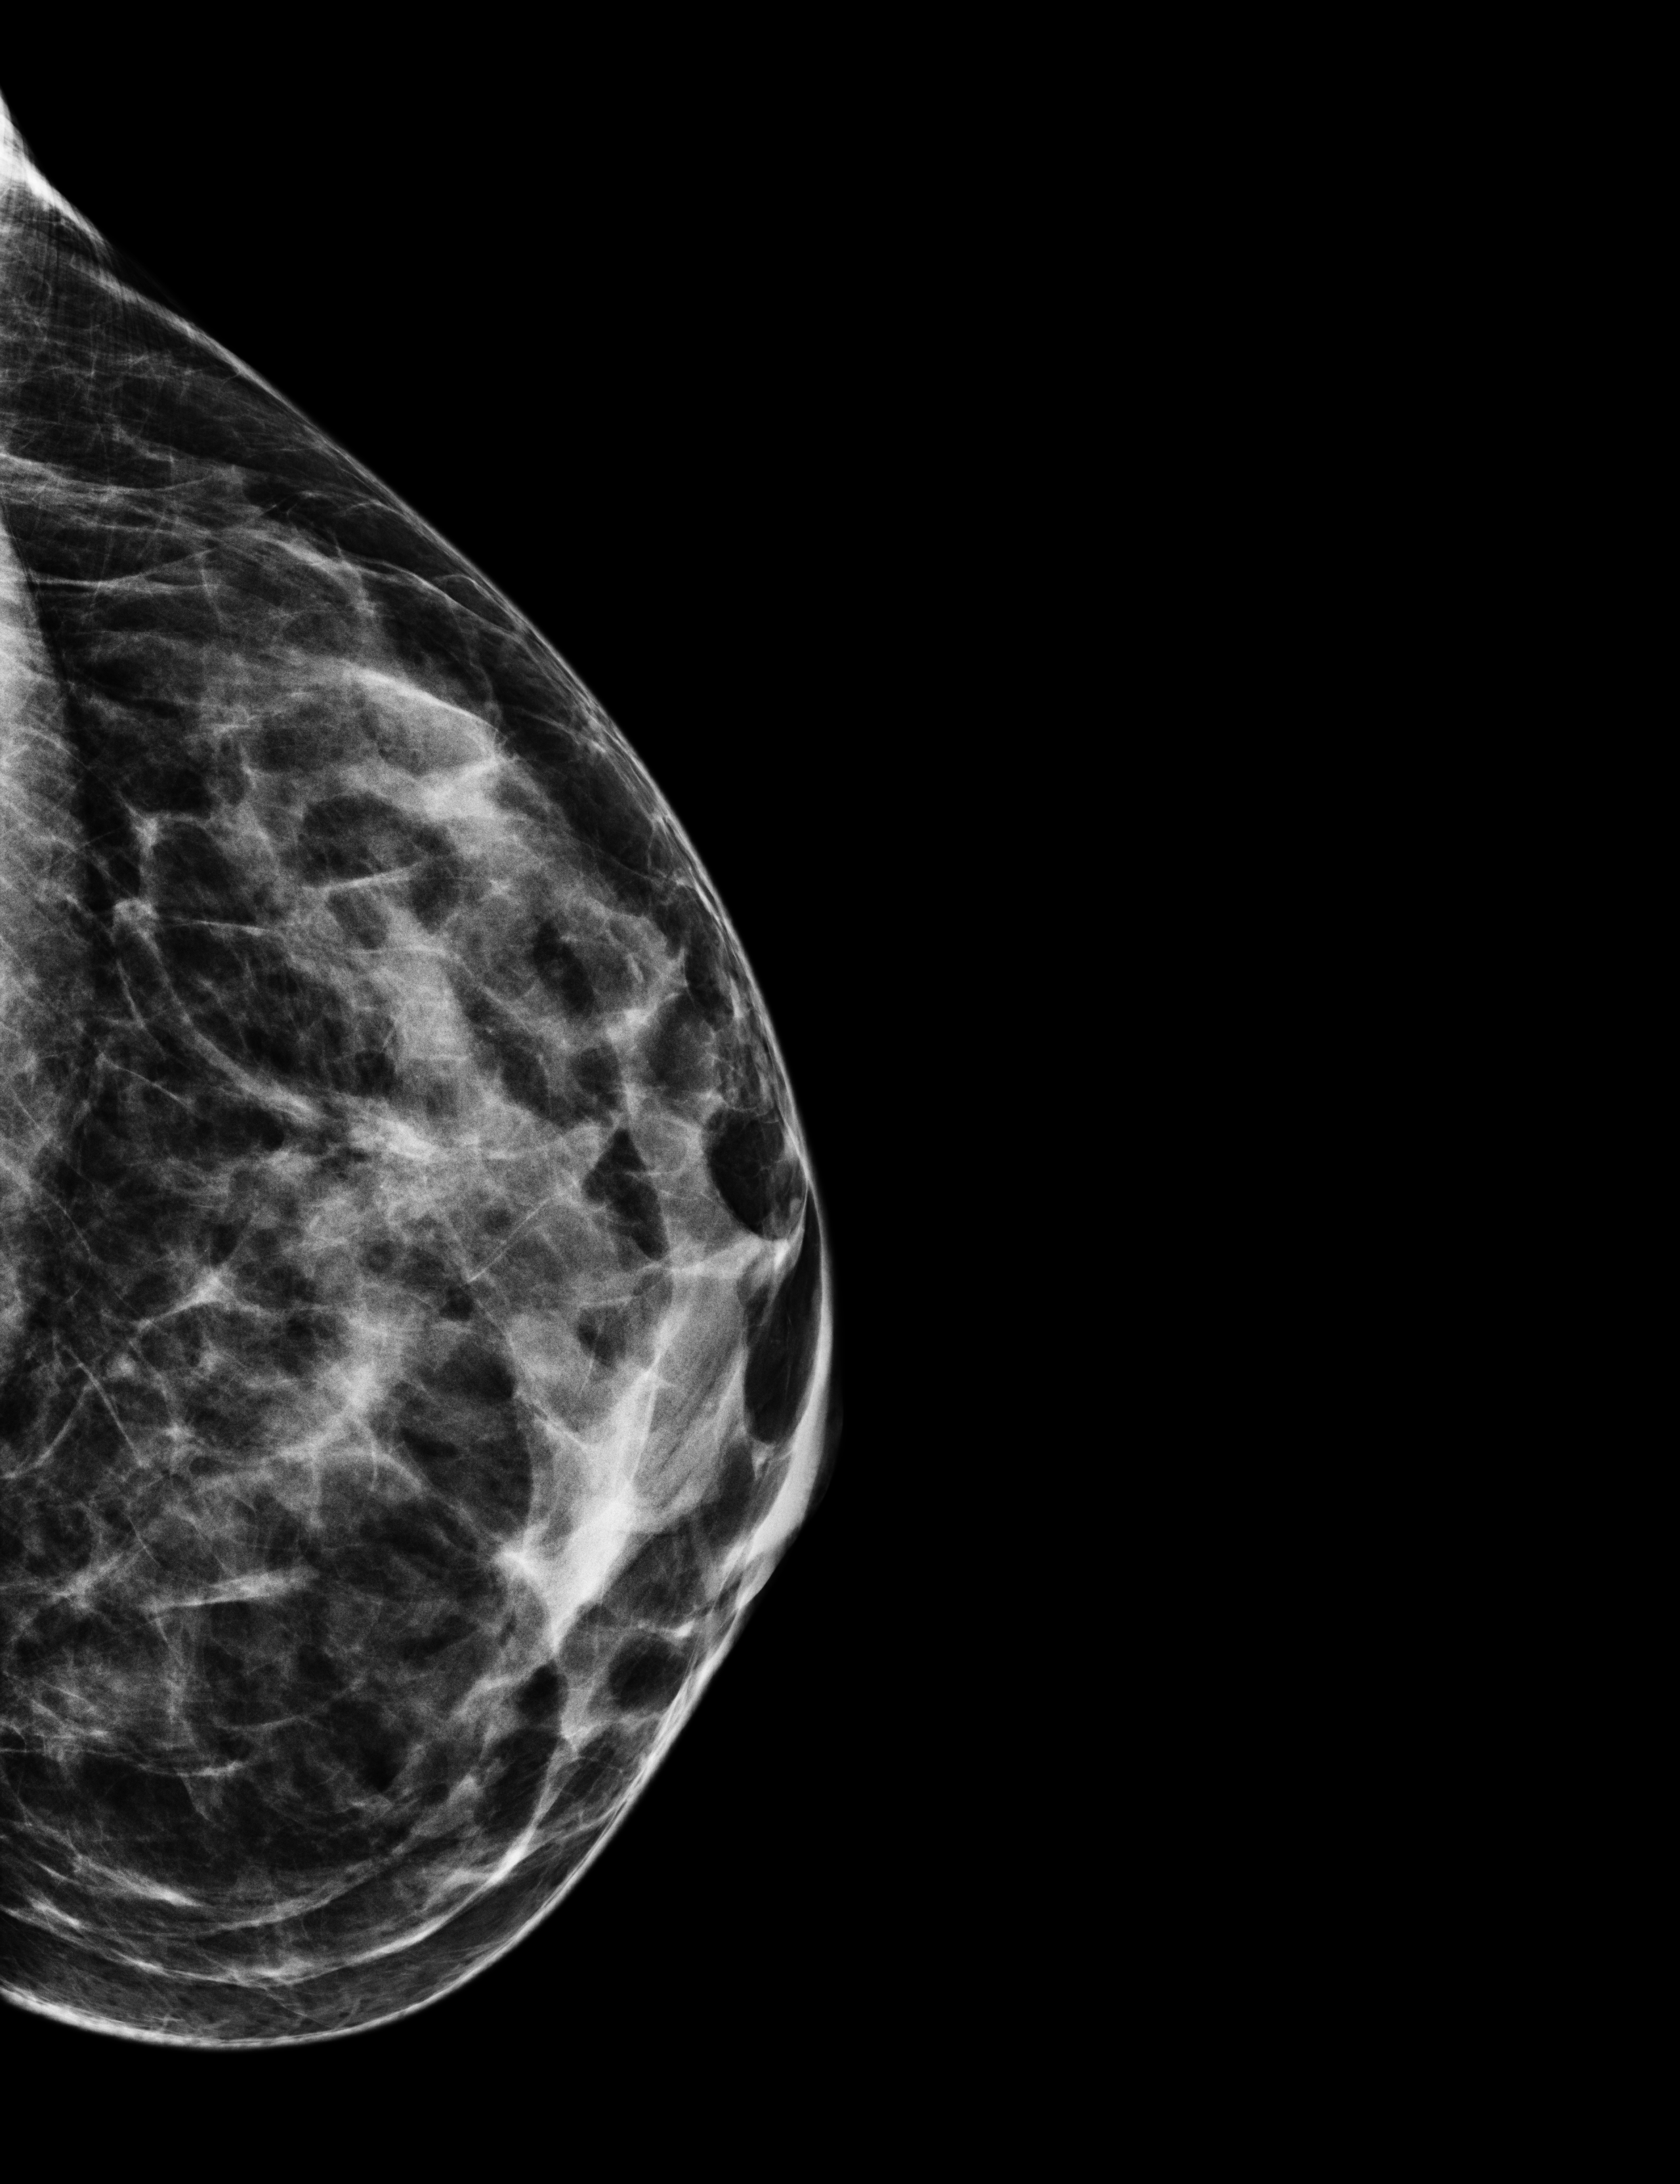
Digital mammogram (FFDM); left breast; exaggerated CC view (lateral); screening examination; compressed breast thickness 48 mm; system: Selenia Dimensions. Patient aged 44 years (female).
- BI-RADS breast density category at the screening exam (both breasts, scale 1–4): 4
- final BI-RADS category for the screening round (tomosynthesis exam, both breasts): category 1
- recall: no recall after this screen